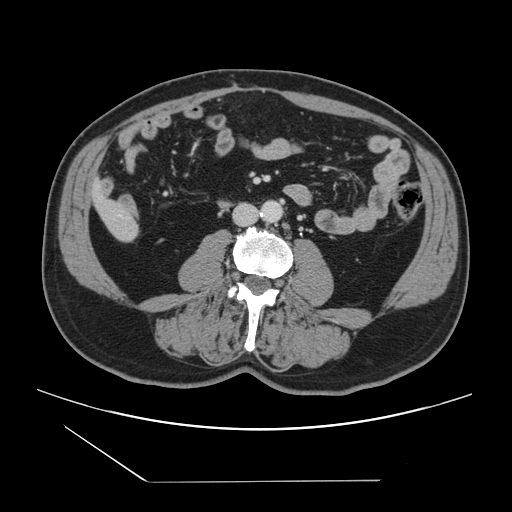
Contrast-enhanced abdominal CT, one axial slice; position 16 of 157 along the scan axis; 120 kVp; intravenous contrast given; soft-tissue window (W 400 / L 40 HU); 512 × 512 image matrix, field of view 407 × 407 mm. Male patient, age 61 years. From the clinical record (not read from this slice): diagnosis: colorectal cancer liver metastases, imaged before liver resection; multiple liver metastases: yes; largest metastasis: 5.5 cm; disease in both lobes: yes.
Outlined on this slice (expert manual segmentation):
- liver: bounding box <95,193,138,242> (left, top, right, bottom; pixels)
- planned liver remnant (the part of the liver to remain after resection): <95,190,120,217>